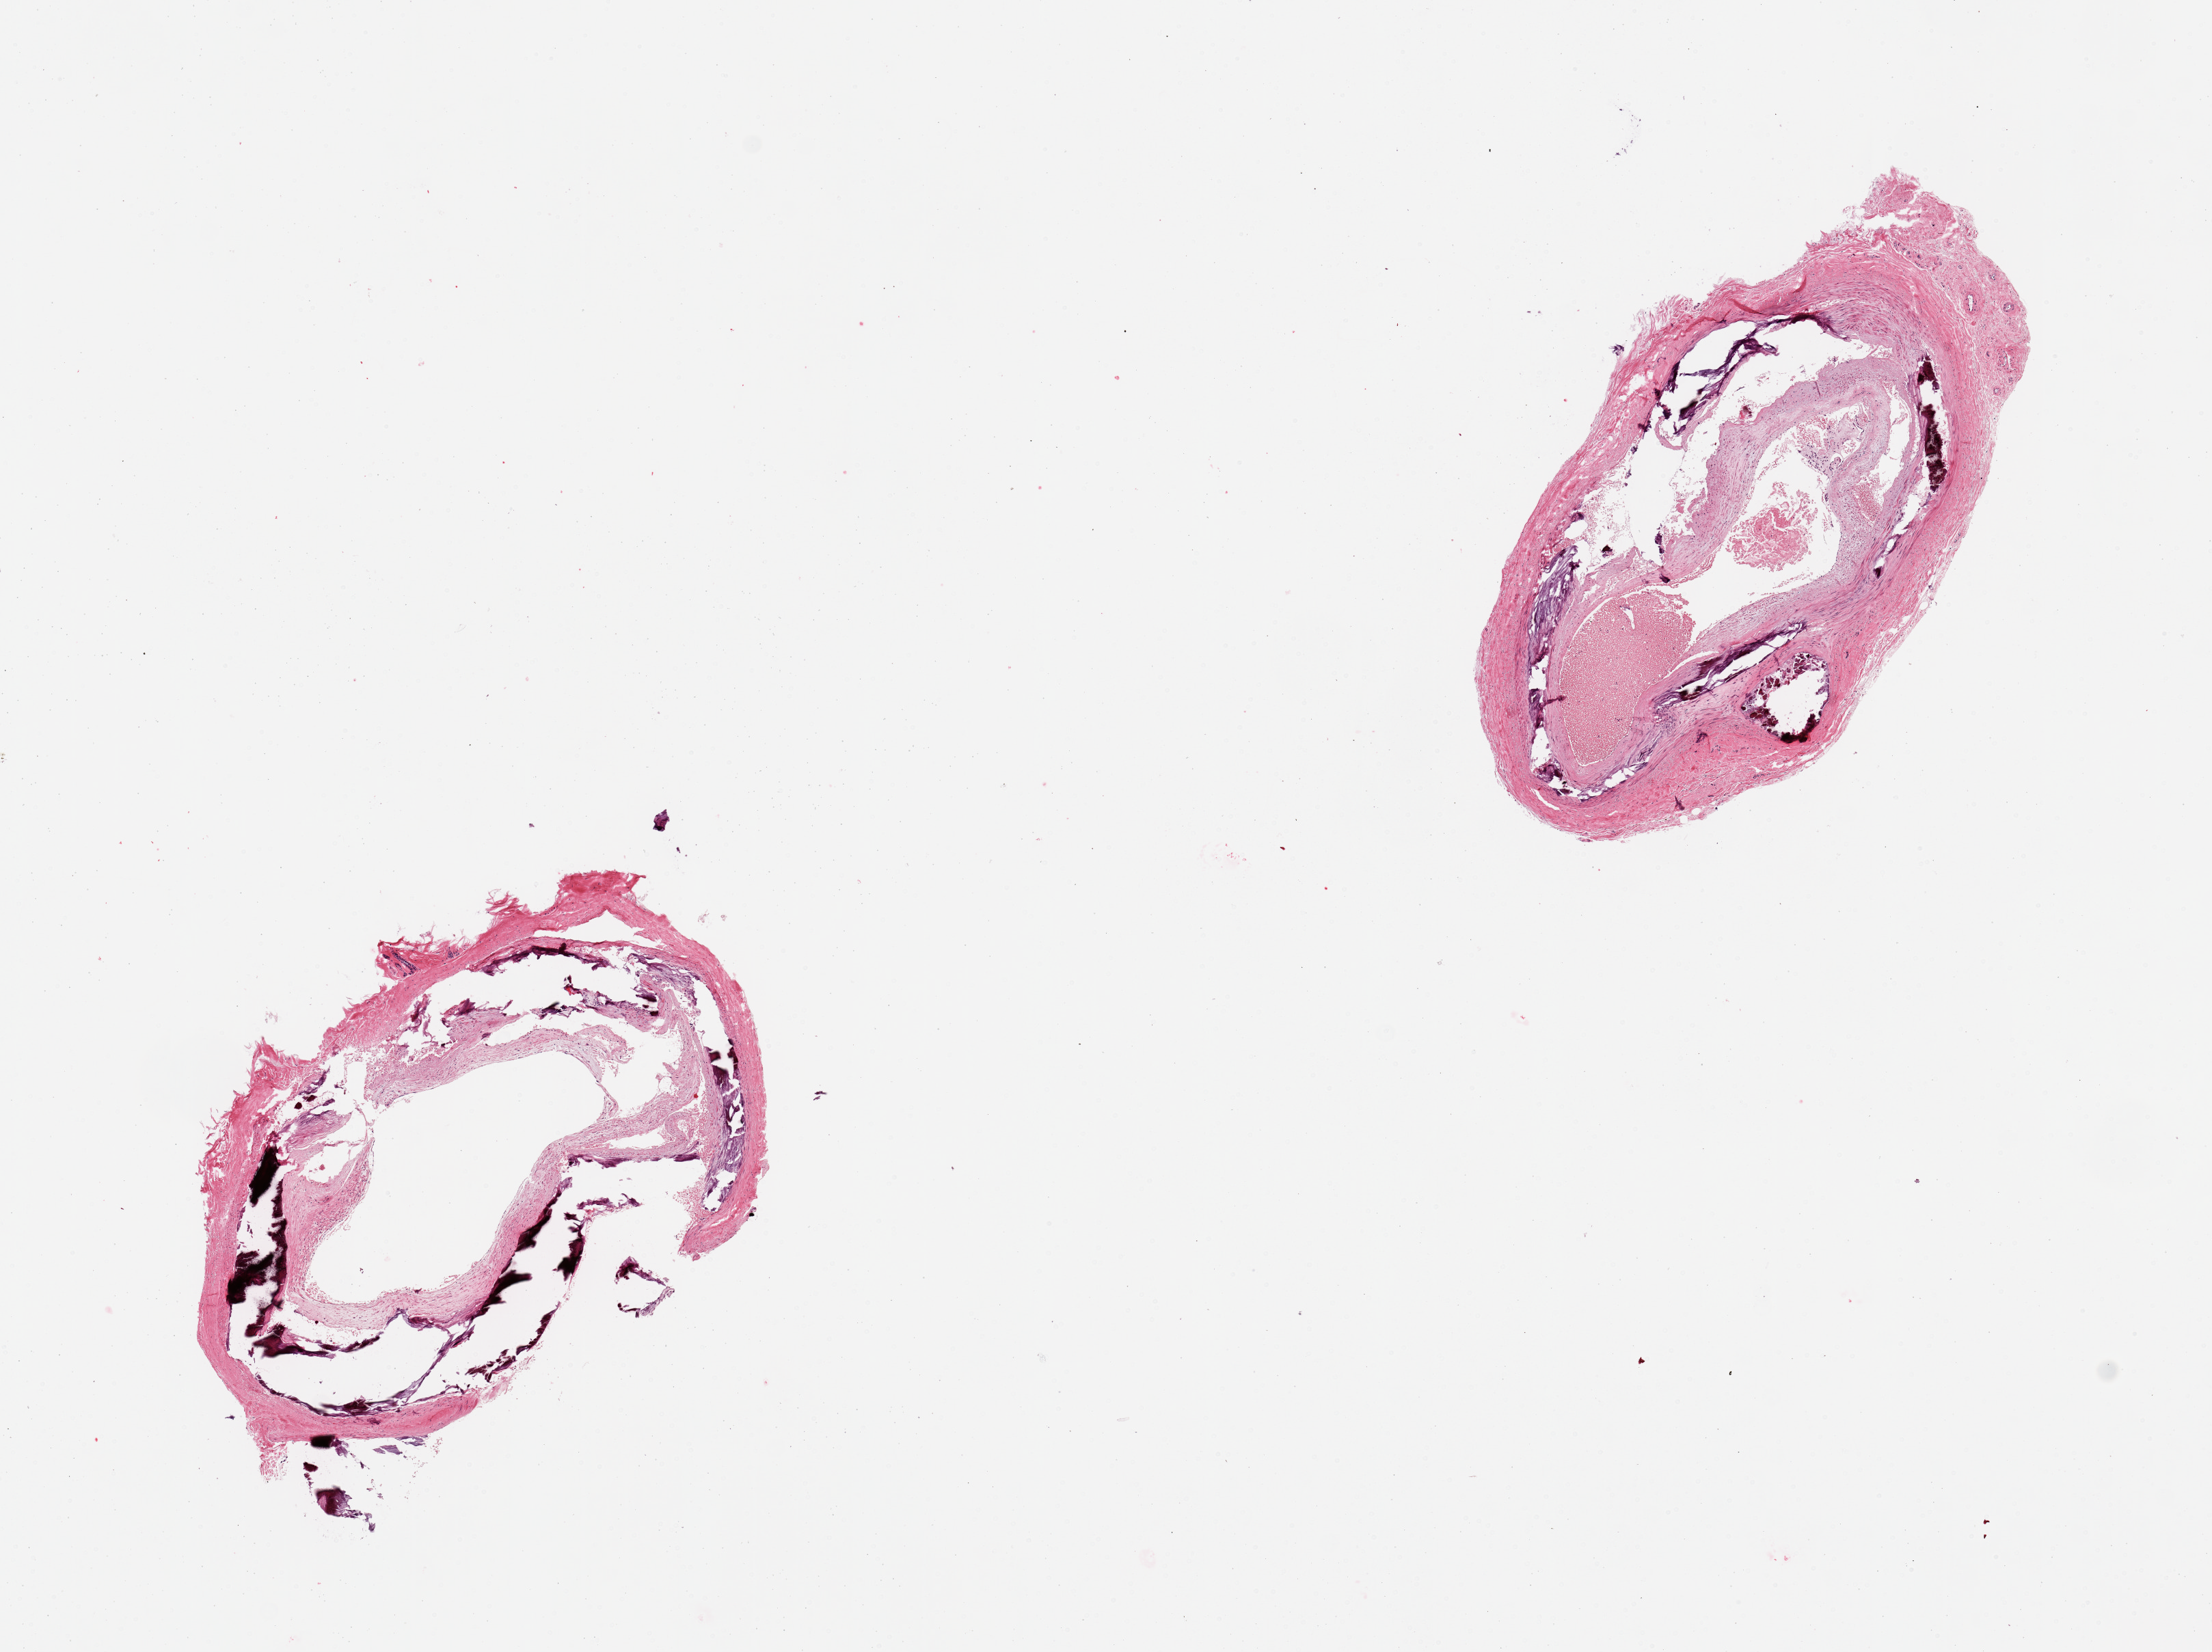
Whole-slide image, haematoxylin and eosin stain — whole scanned area (about 12.8 x 9.6 mm, slide scanned at 20x) shown as a low-resolution overview, PAXgene-fixed, paraffin-embedded tissue, sampled site (target tissue): tibial artery, tissue donor sample. Female donor.
Pathologist's review note for this sample: 2 pieces, good clean specimens, subtotally occlusive atherosis, extensive dystrophic calcification.